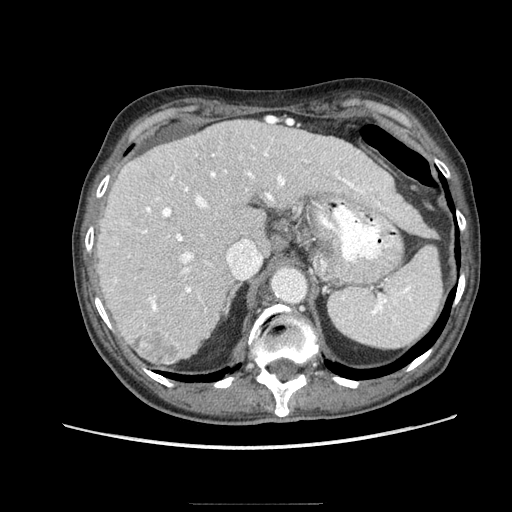
Contrast-enhanced abdominal CT (liver protocol), one axial slice; slice 59 of 83 in the series (ordered by position); reconstruction kernel STANDARD; 140 kVp; soft-tissue window (W 400 / L 40 HU); 2.5 mm slice thickness; 512 × 512 image matrix, field of view 360 × 360 mm. From the clinical record (not read from this slice): diagnosis: hepatocellular carcinoma (patient treated with transarterial chemoembolisation; whether this scan precedes or follows treatment is not stated here); TNM stage (as recorded): Stage-I; Child-Pugh class: A; tumour differentiation: moderately differentiated; tumour nodularity: uninodular.
Annotated regions visible in this slice (semi-automatic segmentation, software-assisted and operator-edited):
- liver parenchyma outside the tumour (the mass and vessels are separate outlines, so this box may not span the whole liver): bounding box [x1, y1, x2, y2] px = [96, 120, 421, 364]
- mass: [131, 330, 178, 364]
- liver vessels: [115, 146, 388, 312]